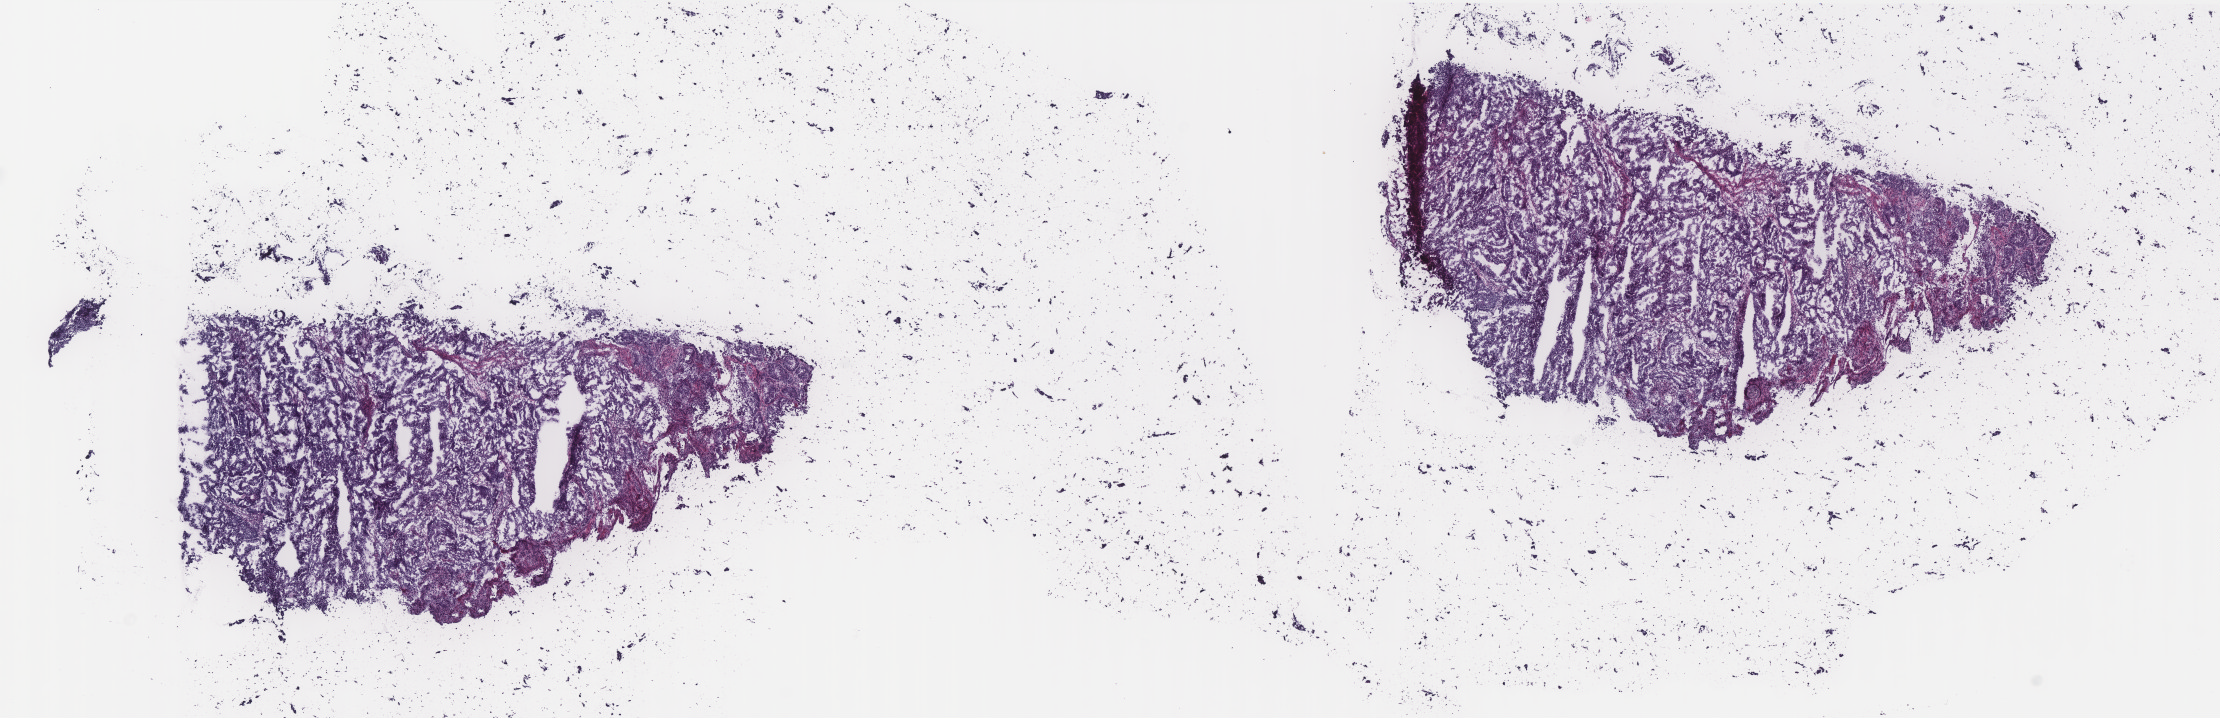
Whole-slide histology image, Hematoxylin and eosin (H&E) stained, shown as a low-resolution overview of the whole scanned area (about 17.8 x 5.8 mm, from a 40x scan); frozen section from the top of the tissue portion; sample: primary tumour, uterus. Female, age 54 years at initial diagnosis. Histologic grade: G1 (well differentiated). Slide review estimates, as recorded: tumour cells 85%, tumour nuclei 85%, normal cells 0%, stromal cells 15%, necrosis 0%. Infiltration values recorded for this section: lymphocyte infiltration 20%, monocyte infiltration 3%, neutrophil infiltration 5%.
- FIGO stage: IA
- histologic diagnosis: Endometrioid adenocarcinoma, NOS (endometrium)
- lymph nodes positive (case pathology): 0 of 32 examined